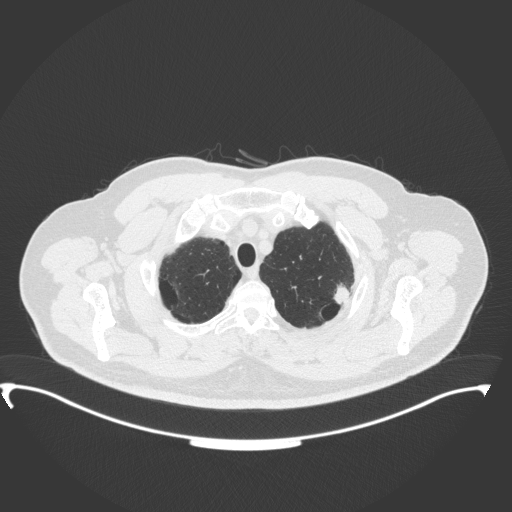
Chest CT, one axial slice. Slice 320 of 350 in the series (ordered by position). 120 kVp. Lung window (W 1500 / L -600 HU). 512 × 512 image matrix, field of view 459 × 459 mm. Male patient, age 64 years. From the clinical record (not read from this slice): clinical TNM (as recorded): T1c N1 M1.
Annotated regions visible in this slice (rectangle marked by the reading radiologist):
- lung tumour (recorded histology: adenocarcinoma): box from (x=333, y=281) to (x=351, y=308) px